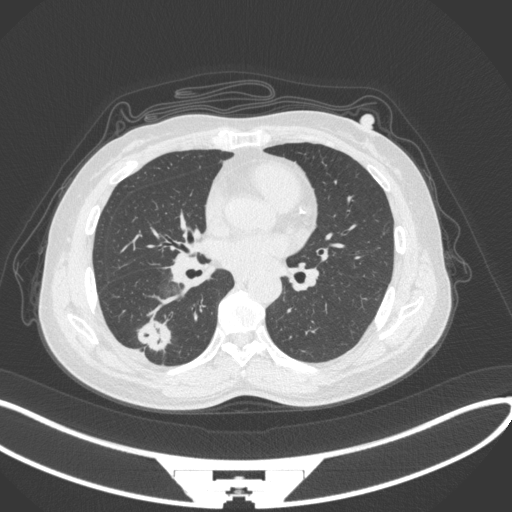
Chest CT, one axial slice; slice 144 of 352 in the series (ordered by position); reconstruction kernel B31f; 120 kVp; lung window (W 1500 / L -600 HU); 512 × 512 image matrix, field of view 400 × 400 mm. Patient: female, 55 years. From the clinical record (not read from this slice): clinical TNM (as recorded): T1c N1 M0.
Annotated regions visible in this slice (rectangle marked by the reading radiologist):
- lung tumour (recorded histology: adenocarcinoma): bounding box (x1, y1, x2, y2) in pixels: (130, 315, 175, 355)